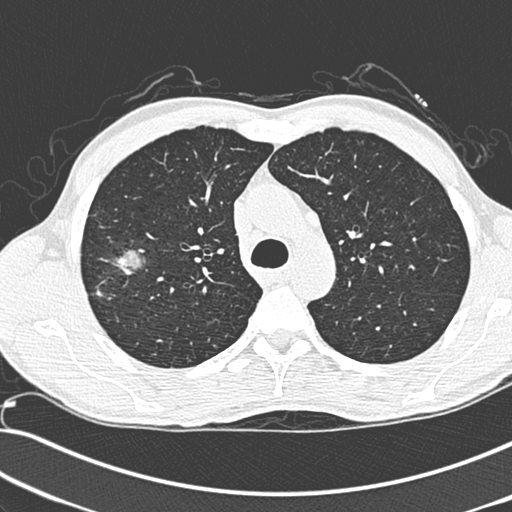
Low-dose screening chest CT, one axial slice; slice 212 of 281 in the series (ordered by position); 120 kVp; lung window (W 1500 / L -600 HU); 1.3 mm slice thickness; 512 × 512 image matrix.
Outlined on this slice (manually delineated by an expert):
- lesion 1 (tumor, upper lobe of right lung): bounding box <113,249,147,275> (left, top, right, bottom; pixels)